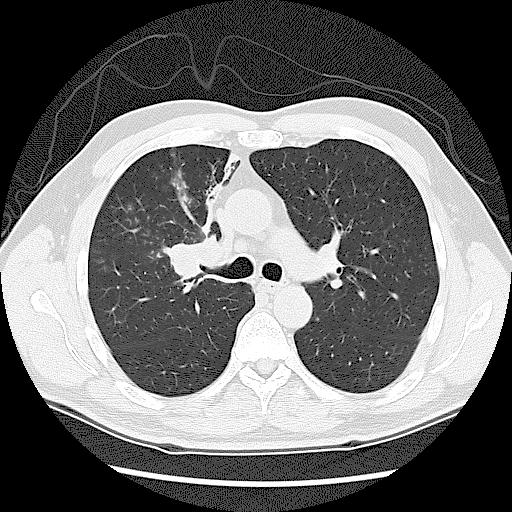
Axial slice from a low-dose chest CT screening exam. First (baseline) screen. Lung window (W 1500 / L -600 HU). 2.5 mm slice thickness. Slice 50 of 131 in the series. Male participant, aged 60 years at enrolment. Current smoker at enrolment.
• Lesion marked by an expert reader, bounding box (x1, y1, x2, y2) in pixels: (158, 221, 242, 315).
• No non-calcified nodule or mass ≥4 mm was recorded by the screening reader at this exam.
• Later outcome: lung cancer diagnosed 41 days after this screen — small cell carcinoma, NOS, right upper lobe, stage IIIA (AJCC 6th edition).